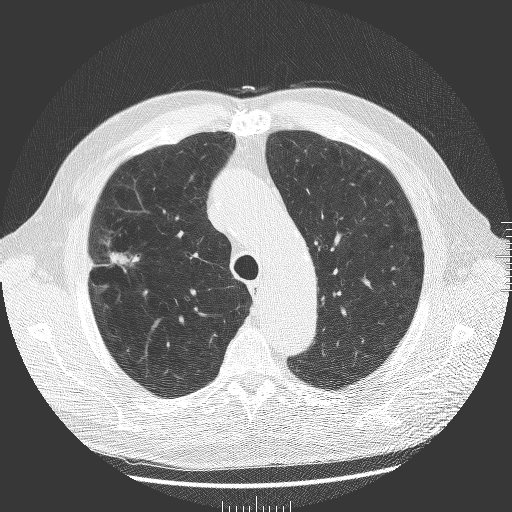
Low-dose screening chest CT, one axial slice. Slice 141 of 181 in the series (ordered by position). Reconstruction kernel BONE. Lung window (W 1500 / L -600 HU). 512 × 512 image matrix, field of view 380 × 380 mm.
Outlined on this slice (outlined manually by an expert reader):
- lesion 1 (tumor, upper lobe of right lung): box from (x=110, y=252) to (x=139, y=266) px